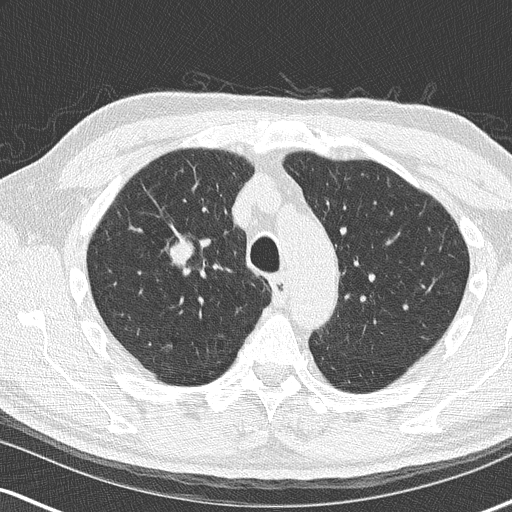
Low-dose screening chest CT, axial slice, second annual screen, lung window (W 1500 / L -600 HU), lung (sharp) reconstruction kernel (B50f), 512 × 512 image matrix, field of view 320 × 320 mm. Male participant, aged 68 years at enrolment. Current smoker at enrolment.
Lesion marked by an expert reader, bounding box (x1, y1, x2, y2) in pixels: (152, 228, 216, 290). The exam's reader record, not a measurement of the box and not confirmed to be the same lesion: non-calcified nodule or mass ≥4 mm, right upper lobe, 18 × 15 mm, smooth margins, soft tissue attenuation, pre-existing on the prior screen: no. Lung cancer was diagnosed 136 days after this screen: small cell carcinoma, NOS, right upper lobe, stage IIIB (AJCC 6th edition), 20 mm at pathology.